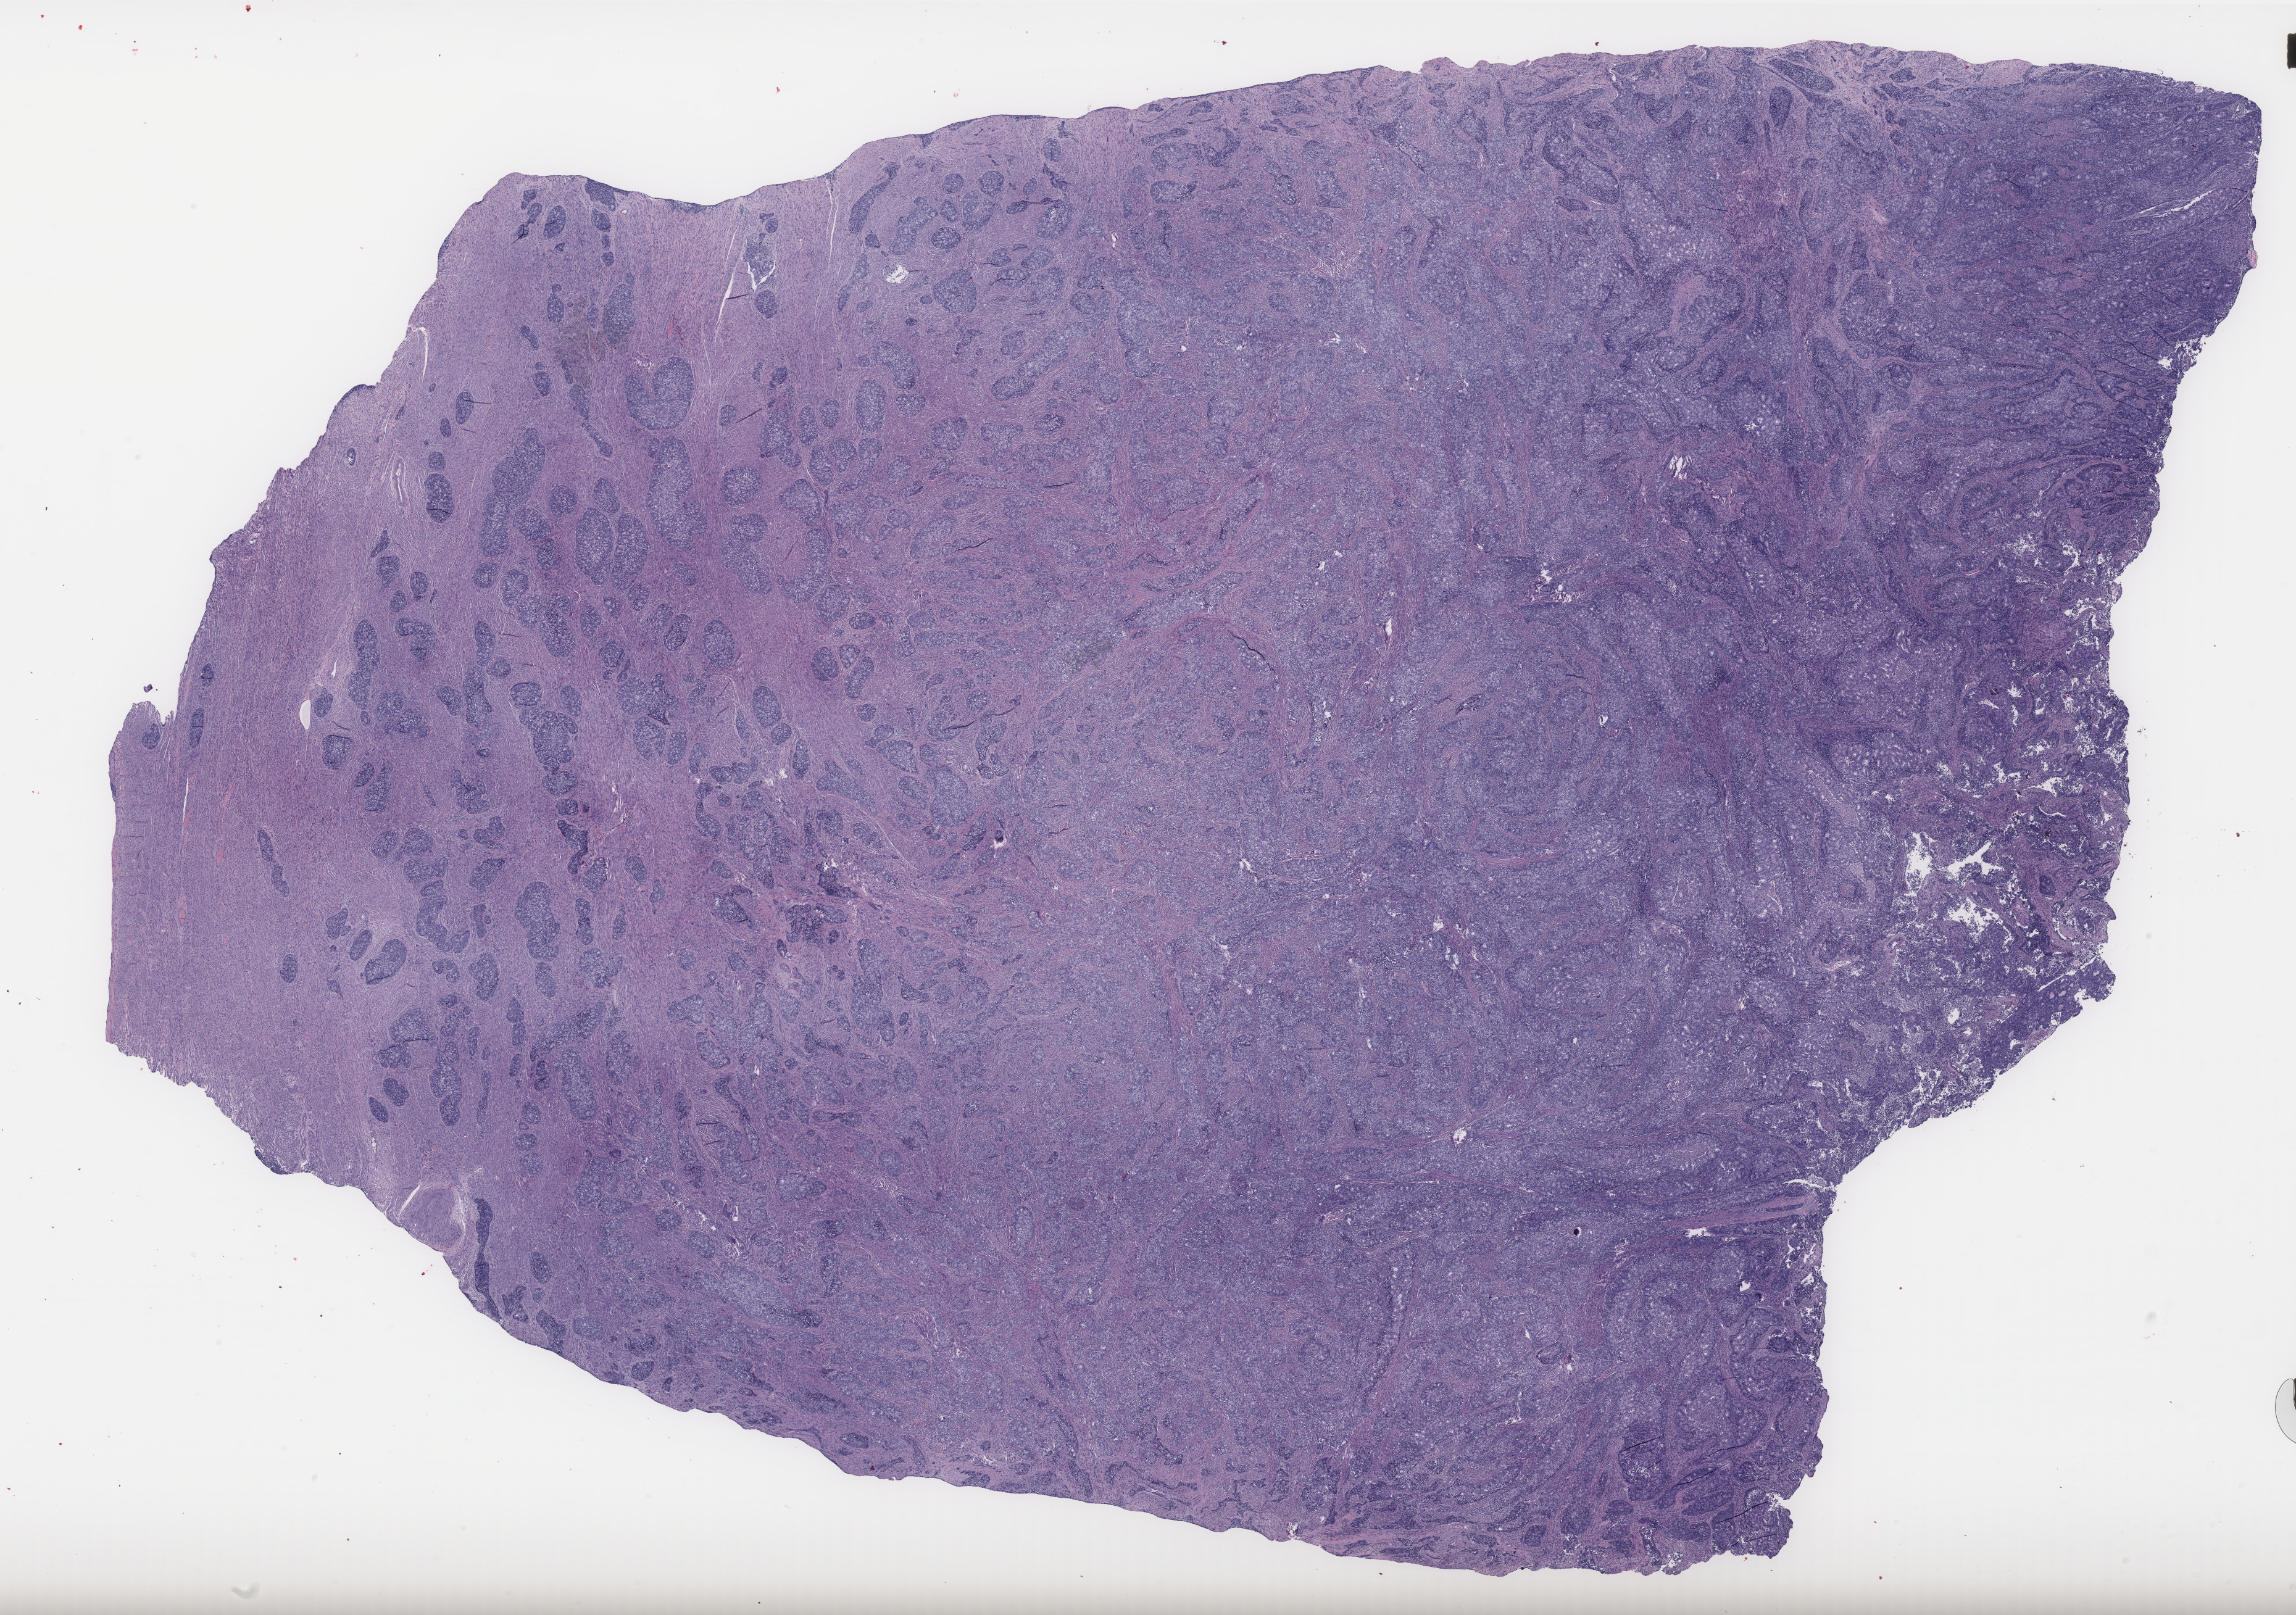
H&E-stained whole-slide image — low-resolution overview of the scanned area, about 29.8 x 21.0 mm. Formalin-fixed paraffin-embedded (FFPE) diagnostic section. Primary tumour sample from the uterus. Female patient; age at initial diagnosis 68 years.
Pathologic diagnosis: Endometrioid adenocarcinoma, NOS.